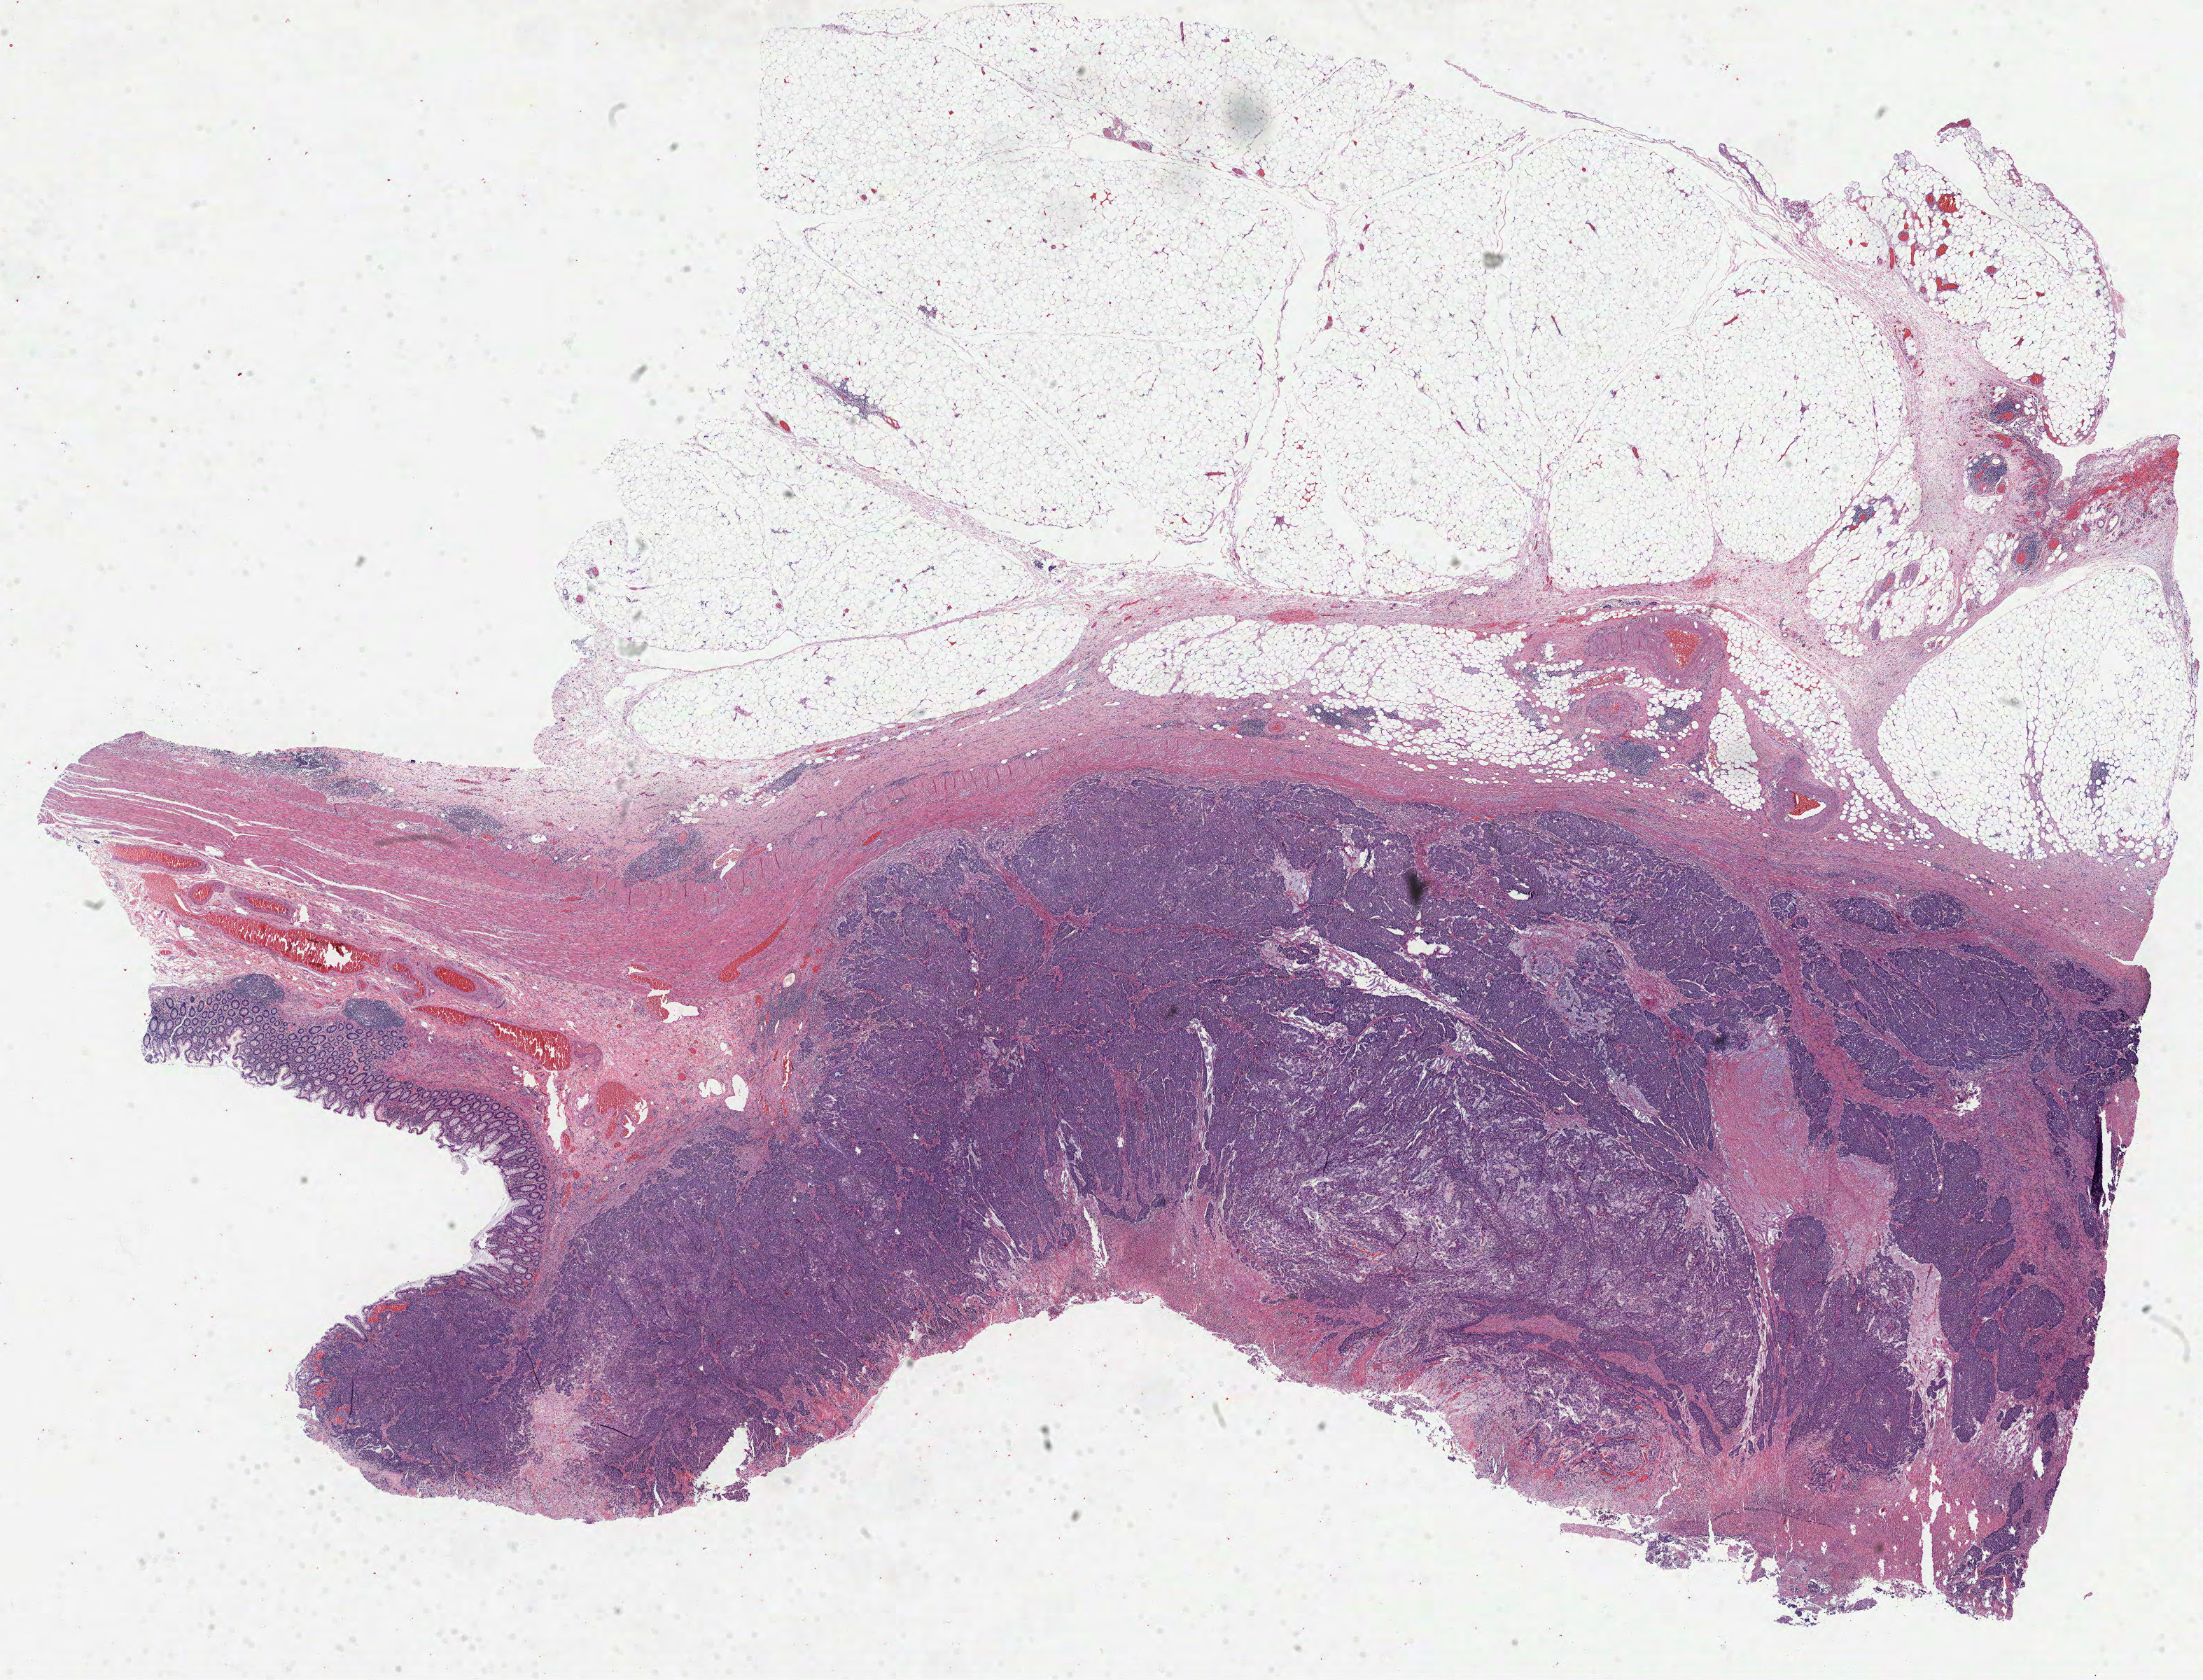
Digitized Hematoxylin and eosin (H&E) stained tissue section (whole slide) — shown as a low-resolution overview of the whole scanned area (about 25.4 x 19.4 mm, from a 40x scan). Formalin-fixed paraffin-embedded (FFPE) diagnostic section. Primary tumour sample from the colon. Patient: female, age at initial diagnosis 77 years.
AJCC pathologic stage: II (5th edition). Diagnosis: Adenocarcinoma, NOS (ascending colon).